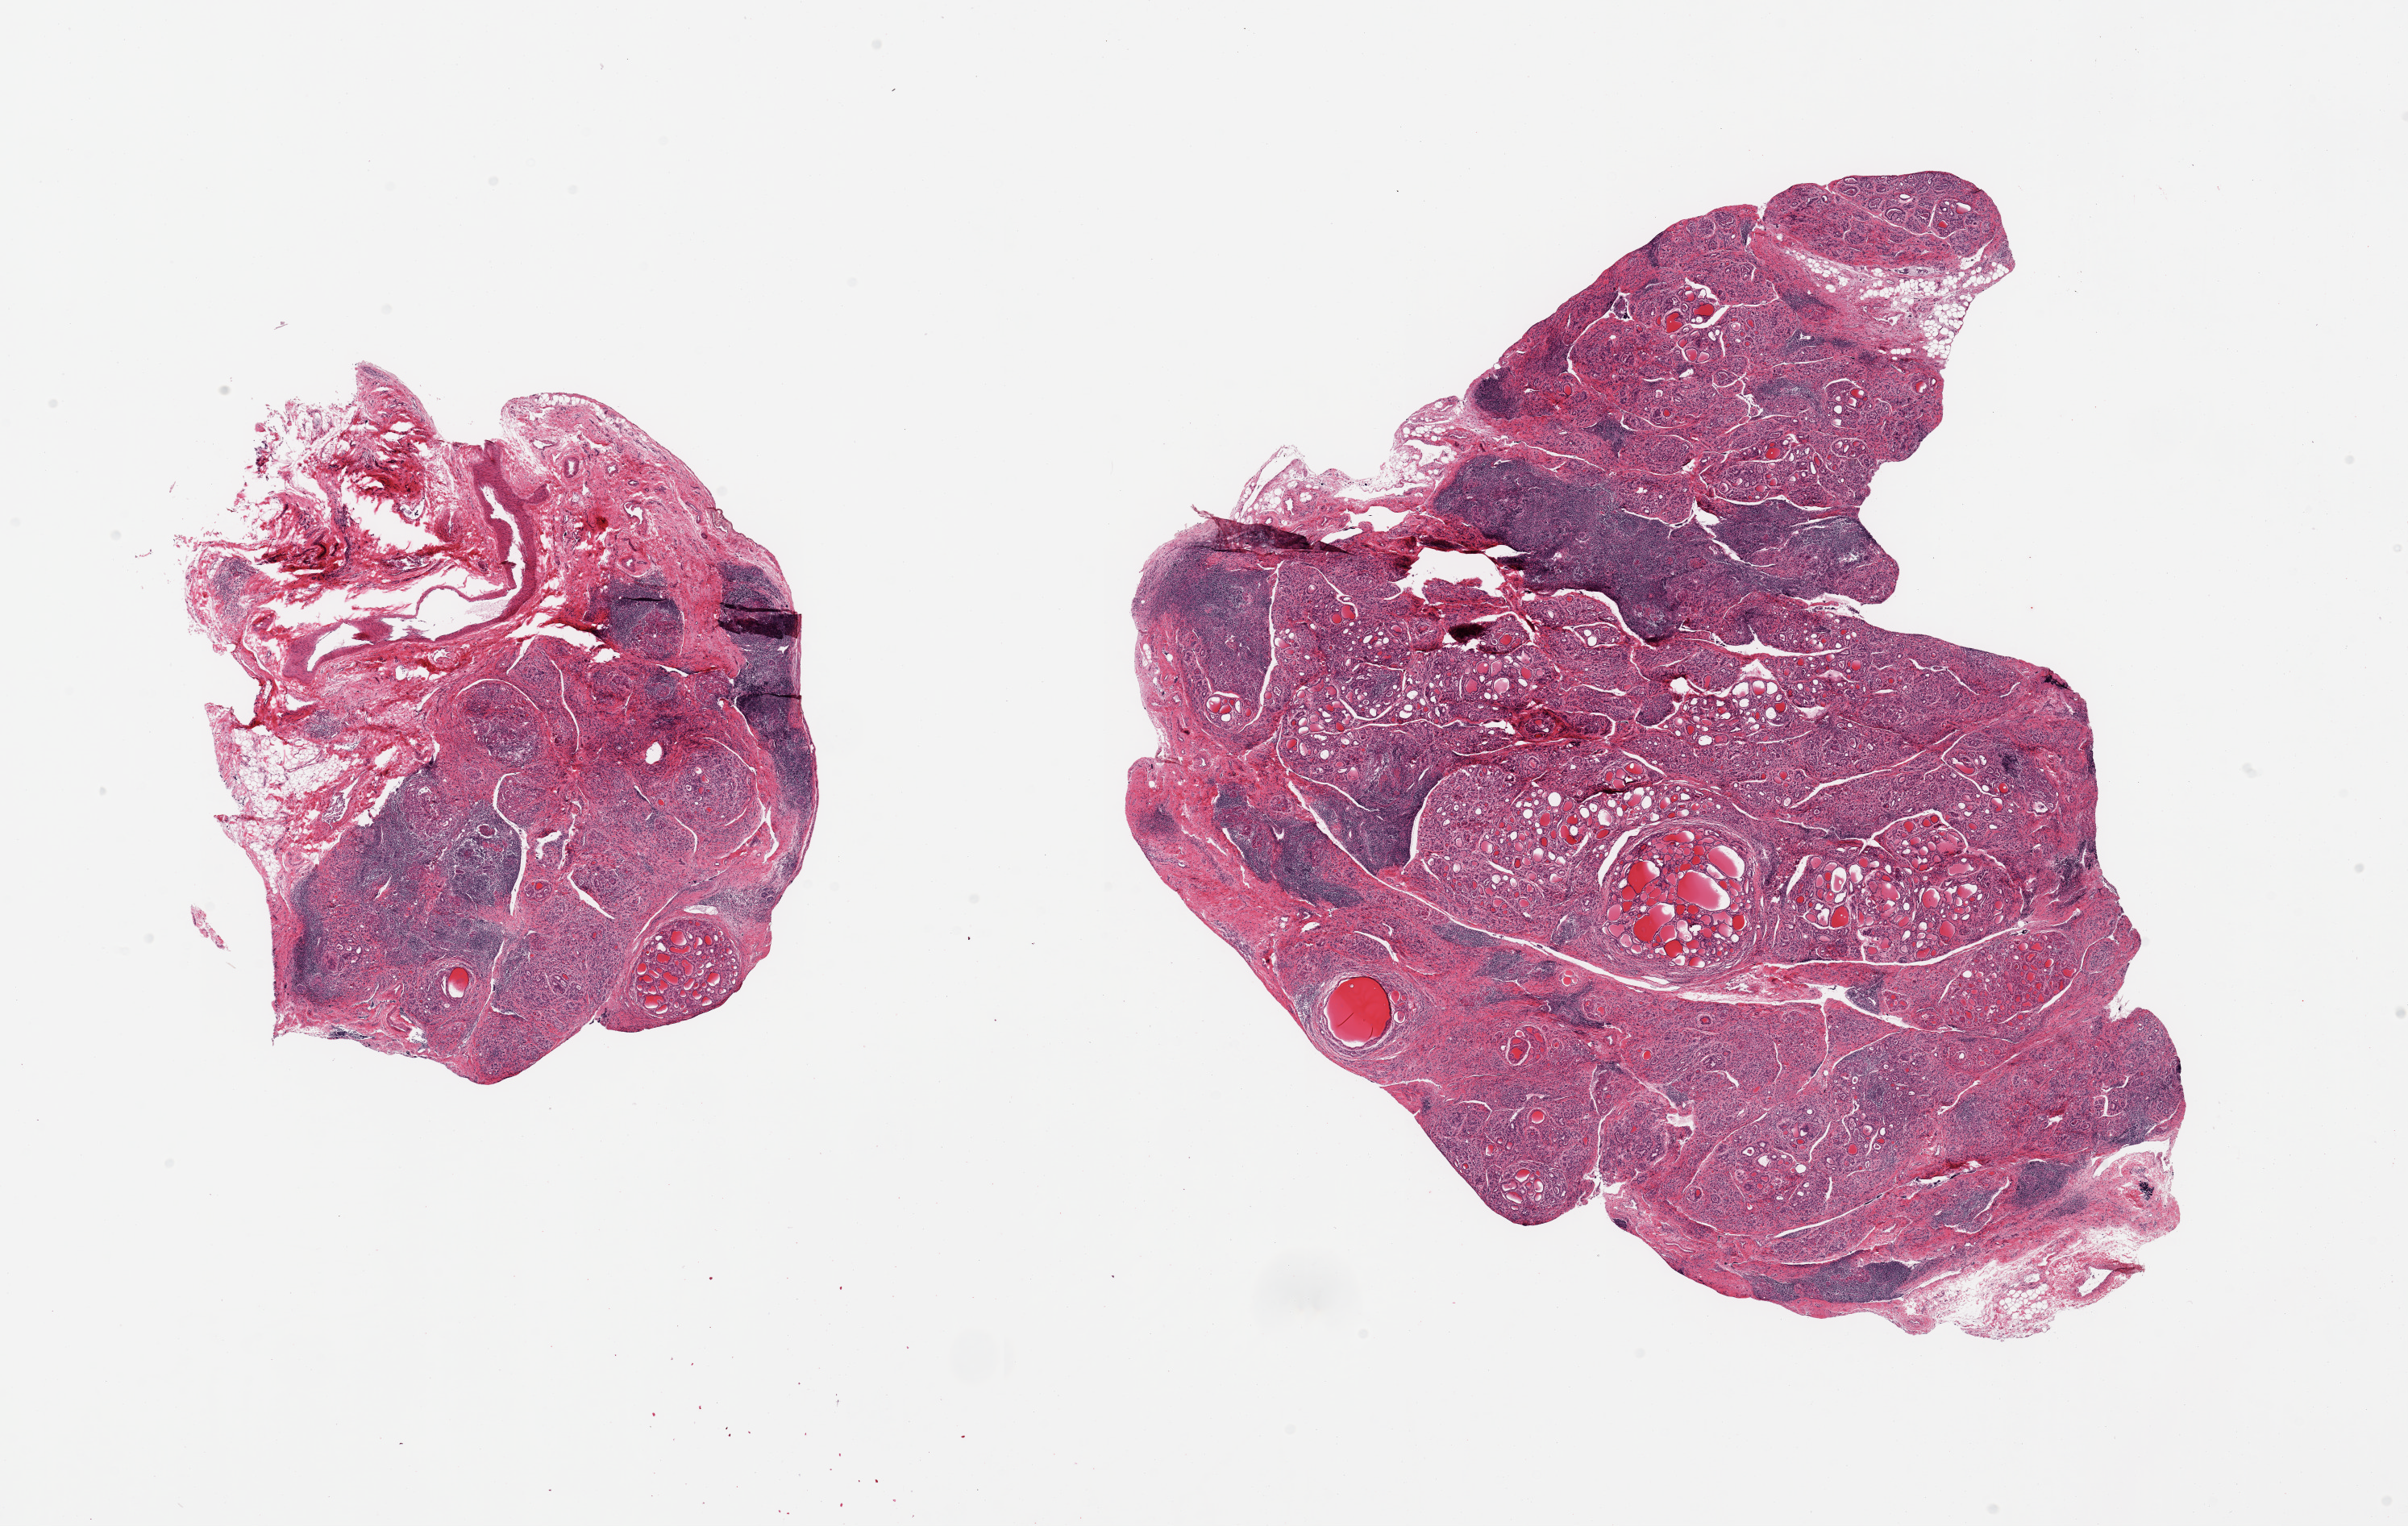
Digitized H&E-stained section — low-resolution overview of the scanned area, about 23.6 x 15.0 mm, PAXgene-fixed, paraffin-embedded tissue, section of thyroid (target tissue), tissue donor sample. Donor: female.
* pathologist's review note for this sample: 2 pieces; moderate lymphocytic (Hashimoto) thyroiditis; 1 piece has 40% fibrofatty external content